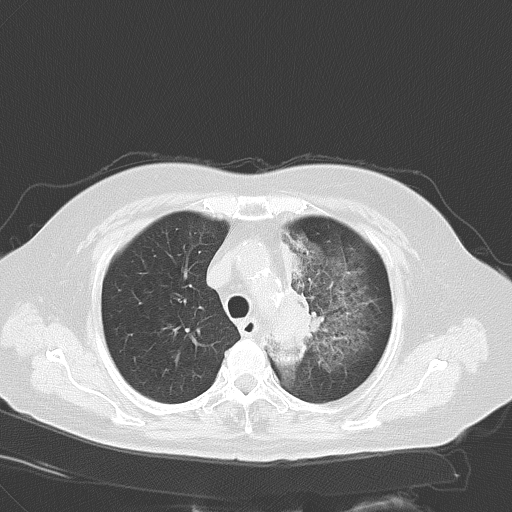
Chest CT, one axial slice. Position 43 of 56 along the scan axis. Reconstruction kernel B70f. 120 kVp. Lung window (W 1500 / L -600 HU). 512 × 512 image matrix. Patient: female, 65 years. From the clinical record (not read from this slice): clinical TNM (as recorded): T2b N1 M0.
Outlined on this slice (rectangle marked by the reading radiologist):
- lung tumour (recorded histology: adenocarcinoma): bounding box <288,283,328,355> (left, top, right, bottom; pixels)